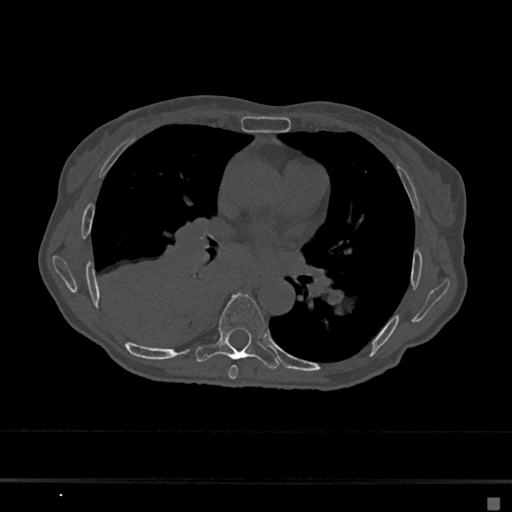
CT including the spine, one axial slice. Slice 380 of 797 in the series (ordered by position). 120 kVp. Bone window (W 1800 / L 400 HU). 512 × 512 image matrix, field of view 360 × 360 mm. Female patient, age 68 years. Case-level facts recorded for this patient, not image findings: primary cancer: renal.
Annotated regions visible in this slice (semi-automatic segmentation, software-assisted and operator-edited):
- T6 vertebra: bounding box [x1, y1, x2, y2] px = [228, 365, 238, 380]
- T7 vertebra: [195, 293, 279, 369]